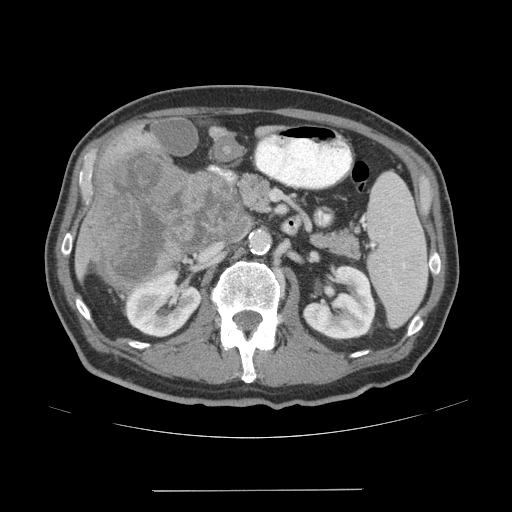
Contrast-enhanced abdominal CT (liver protocol), one axial slice; position 17 of 77 along the scan axis; 140 kVp; soft-tissue window (W 400 / L 40 HU); 2.5 mm slice thickness; 512 × 512 image matrix, field of view 400 × 400 mm. Case-level facts recorded for this patient, not image findings: diagnosis: hepatocellular carcinoma (patient treated with transarterial chemoembolisation; whether this scan precedes or follows treatment is not stated here); TNM stage (as recorded): Stage-IVA; Child-Pugh class: A; tumour differentiation: well differentiated; tumour nodularity: uninodular.
Outlined on this slice (semi-automatic segmentation, software-assisted and operator-edited):
- liver parenchyma outside the tumour (the mass and vessels are separate outlines, so this box may not span the whole liver): bounding box (x1, y1, x2, y2) in pixels: (74, 130, 177, 298)
- mass: (89, 145, 238, 292)